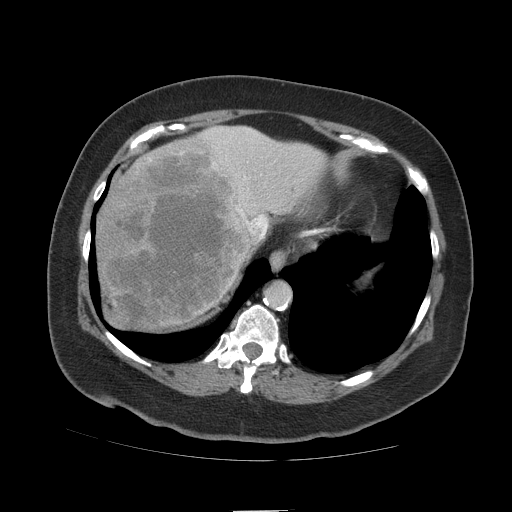
Contrast-enhanced abdominal CT (liver protocol), one axial slice. Soft-tissue window (W 400 / L 40 HU). 512 × 512 image matrix, field of view 420 × 420 mm. Case-level facts recorded for this patient, not image findings: diagnosis: hepatocellular carcinoma (patient treated with transarterial chemoembolisation; whether this scan precedes or follows treatment is not stated here); TNM stage (as recorded): Stage-IVB; Child-Pugh class: A; tumour differentiation: poorly differentiated.
Annotated regions visible in this slice (semi-automatic segmentation, software-assisted and operator-edited):
- abdominal aorta: bounding box <266,282,291,307> (left, top, right, bottom; pixels)
- liver parenchyma outside the tumour (the mass and vessels are separate outlines, so this box may not span the whole liver): <98,126,326,328>
- mass: <95,137,255,329>
- liver vessels: <210,129,268,239>